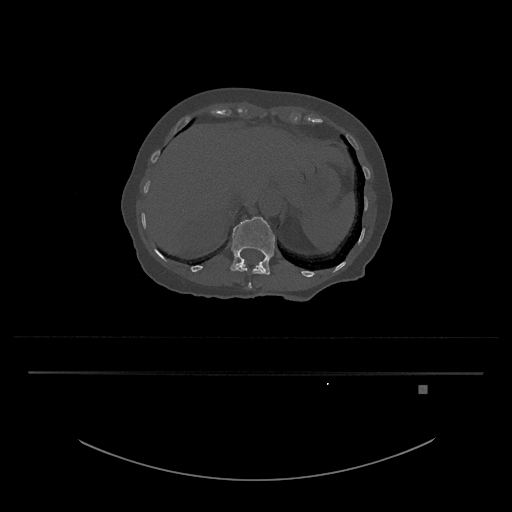
CT including the spine, one axial slice; slice 578 of 797 in the series (ordered by position); reconstruction kernel Br40s/3; 120 kVp; bone window (W 1800 / L 400 HU); 0.5 mm slice thickness; 512 × 512 image matrix, field of view 500 × 500 mm. Patient: female, 57 years. From the clinical record (not read from this slice): primary cancer: cervical.
Structures marked on this image (semi-automatic segmentation, software-assisted and operator-edited):
- L1 vertebra: bounding box [x1, y1, x2, y2] px = [231, 217, 275, 275]
- T12 vertebra: [235, 263, 265, 289]